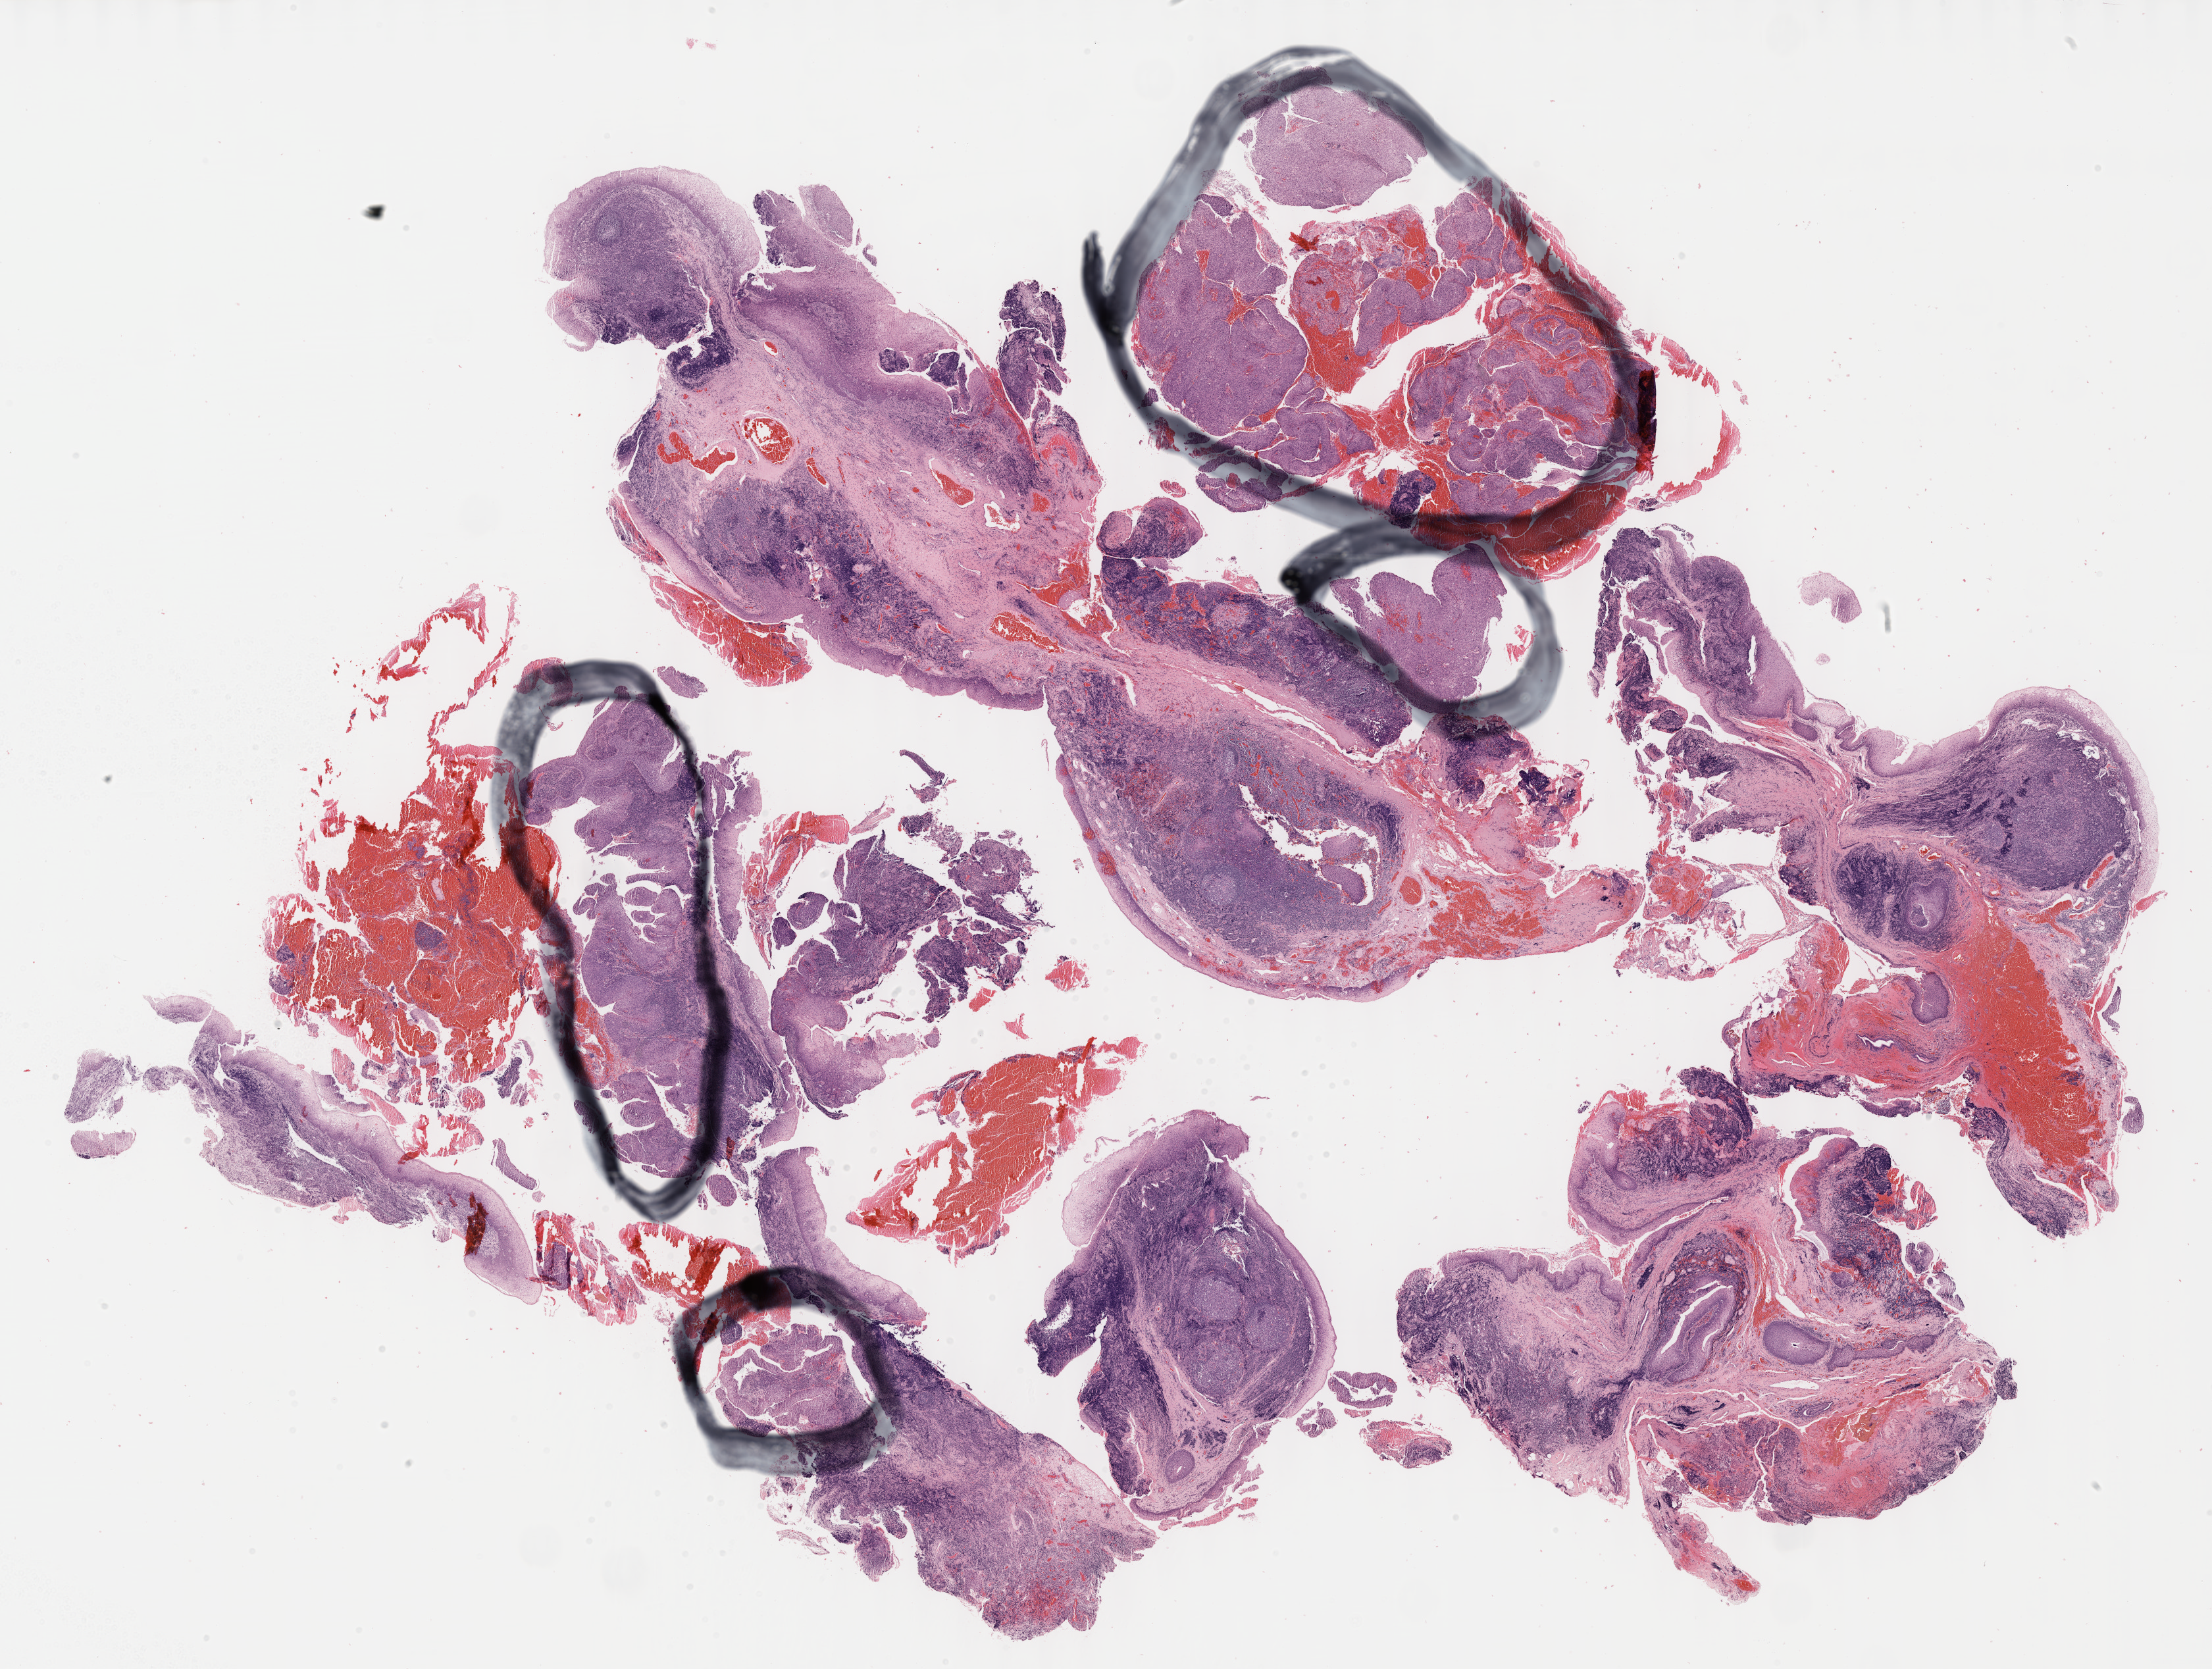
Hematoxylin and eosin (H&E) stained whole-slide image — a low-resolution overview of the entire scanned area, about 27.2 x 20.5 mm (acquisition: 40x scan); formalin-fixed paraffin-embedded (FFPE) diagnostic section; sample: primary tumour, head and neck. Male patient; age at initial diagnosis 47 years. Histologic grade: G4 (undifferentiated).
Pathologic diagnosis: Squamous cell carcinoma, NOS. Laterality: right.